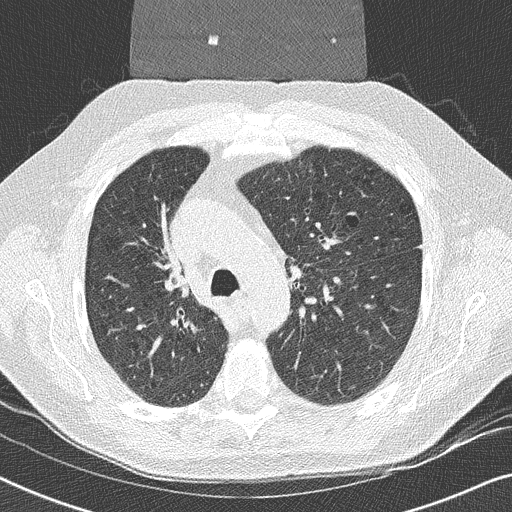
Low-dose screening chest CT, axial slice. Second annual screen. Lung window (W 1500 / L -600 HU). 120 kVp. Male, age 59 years at enrolment. Former smoker at enrolment.
- Expert reader's lesion annotation, bounding box [x1, y1, x2, y2] px = [134, 253, 200, 309].
- Reader record for this screening exam (exam-level; its link to the box is not recorded): non-calcified nodule or mass ≥4 mm, right upper lobe, 17 × 16 mm, smooth margins, soft tissue attenuation, pre-existing on the prior screen: yes.
- Official screen result: positive, other.
- Participant outcome: lung cancer diagnosed 14 days after this screen — squamous cell carcinoma, NOS, right upper lobe, poorly differentiated (G3), stage IIA (AJCC 6th edition), 20 mm at pathology.